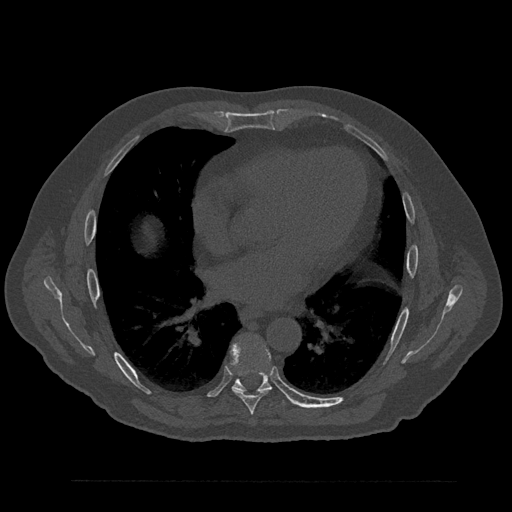
CT including the spine, one axial slice; slice 485 of 797 in the series (ordered by position); reconstruction kernel Br40s/3; 120 kVp; bone window (W 1800 / L 400 HU); 0.5 mm slice thickness; 512 × 512 image matrix, field of view 430 × 430 mm. Male patient, age 61 years. Case-level facts recorded for this patient, not image findings: primary cancer: prostate.
Annotated regions visible in this slice (semi-automatic segmentation, software-assisted and operator-edited):
- T7 vertebra: box from (x=230, y=342) to (x=272, y=415) px
- T8 vertebra: (x=232, y=340)–(x=272, y=392)